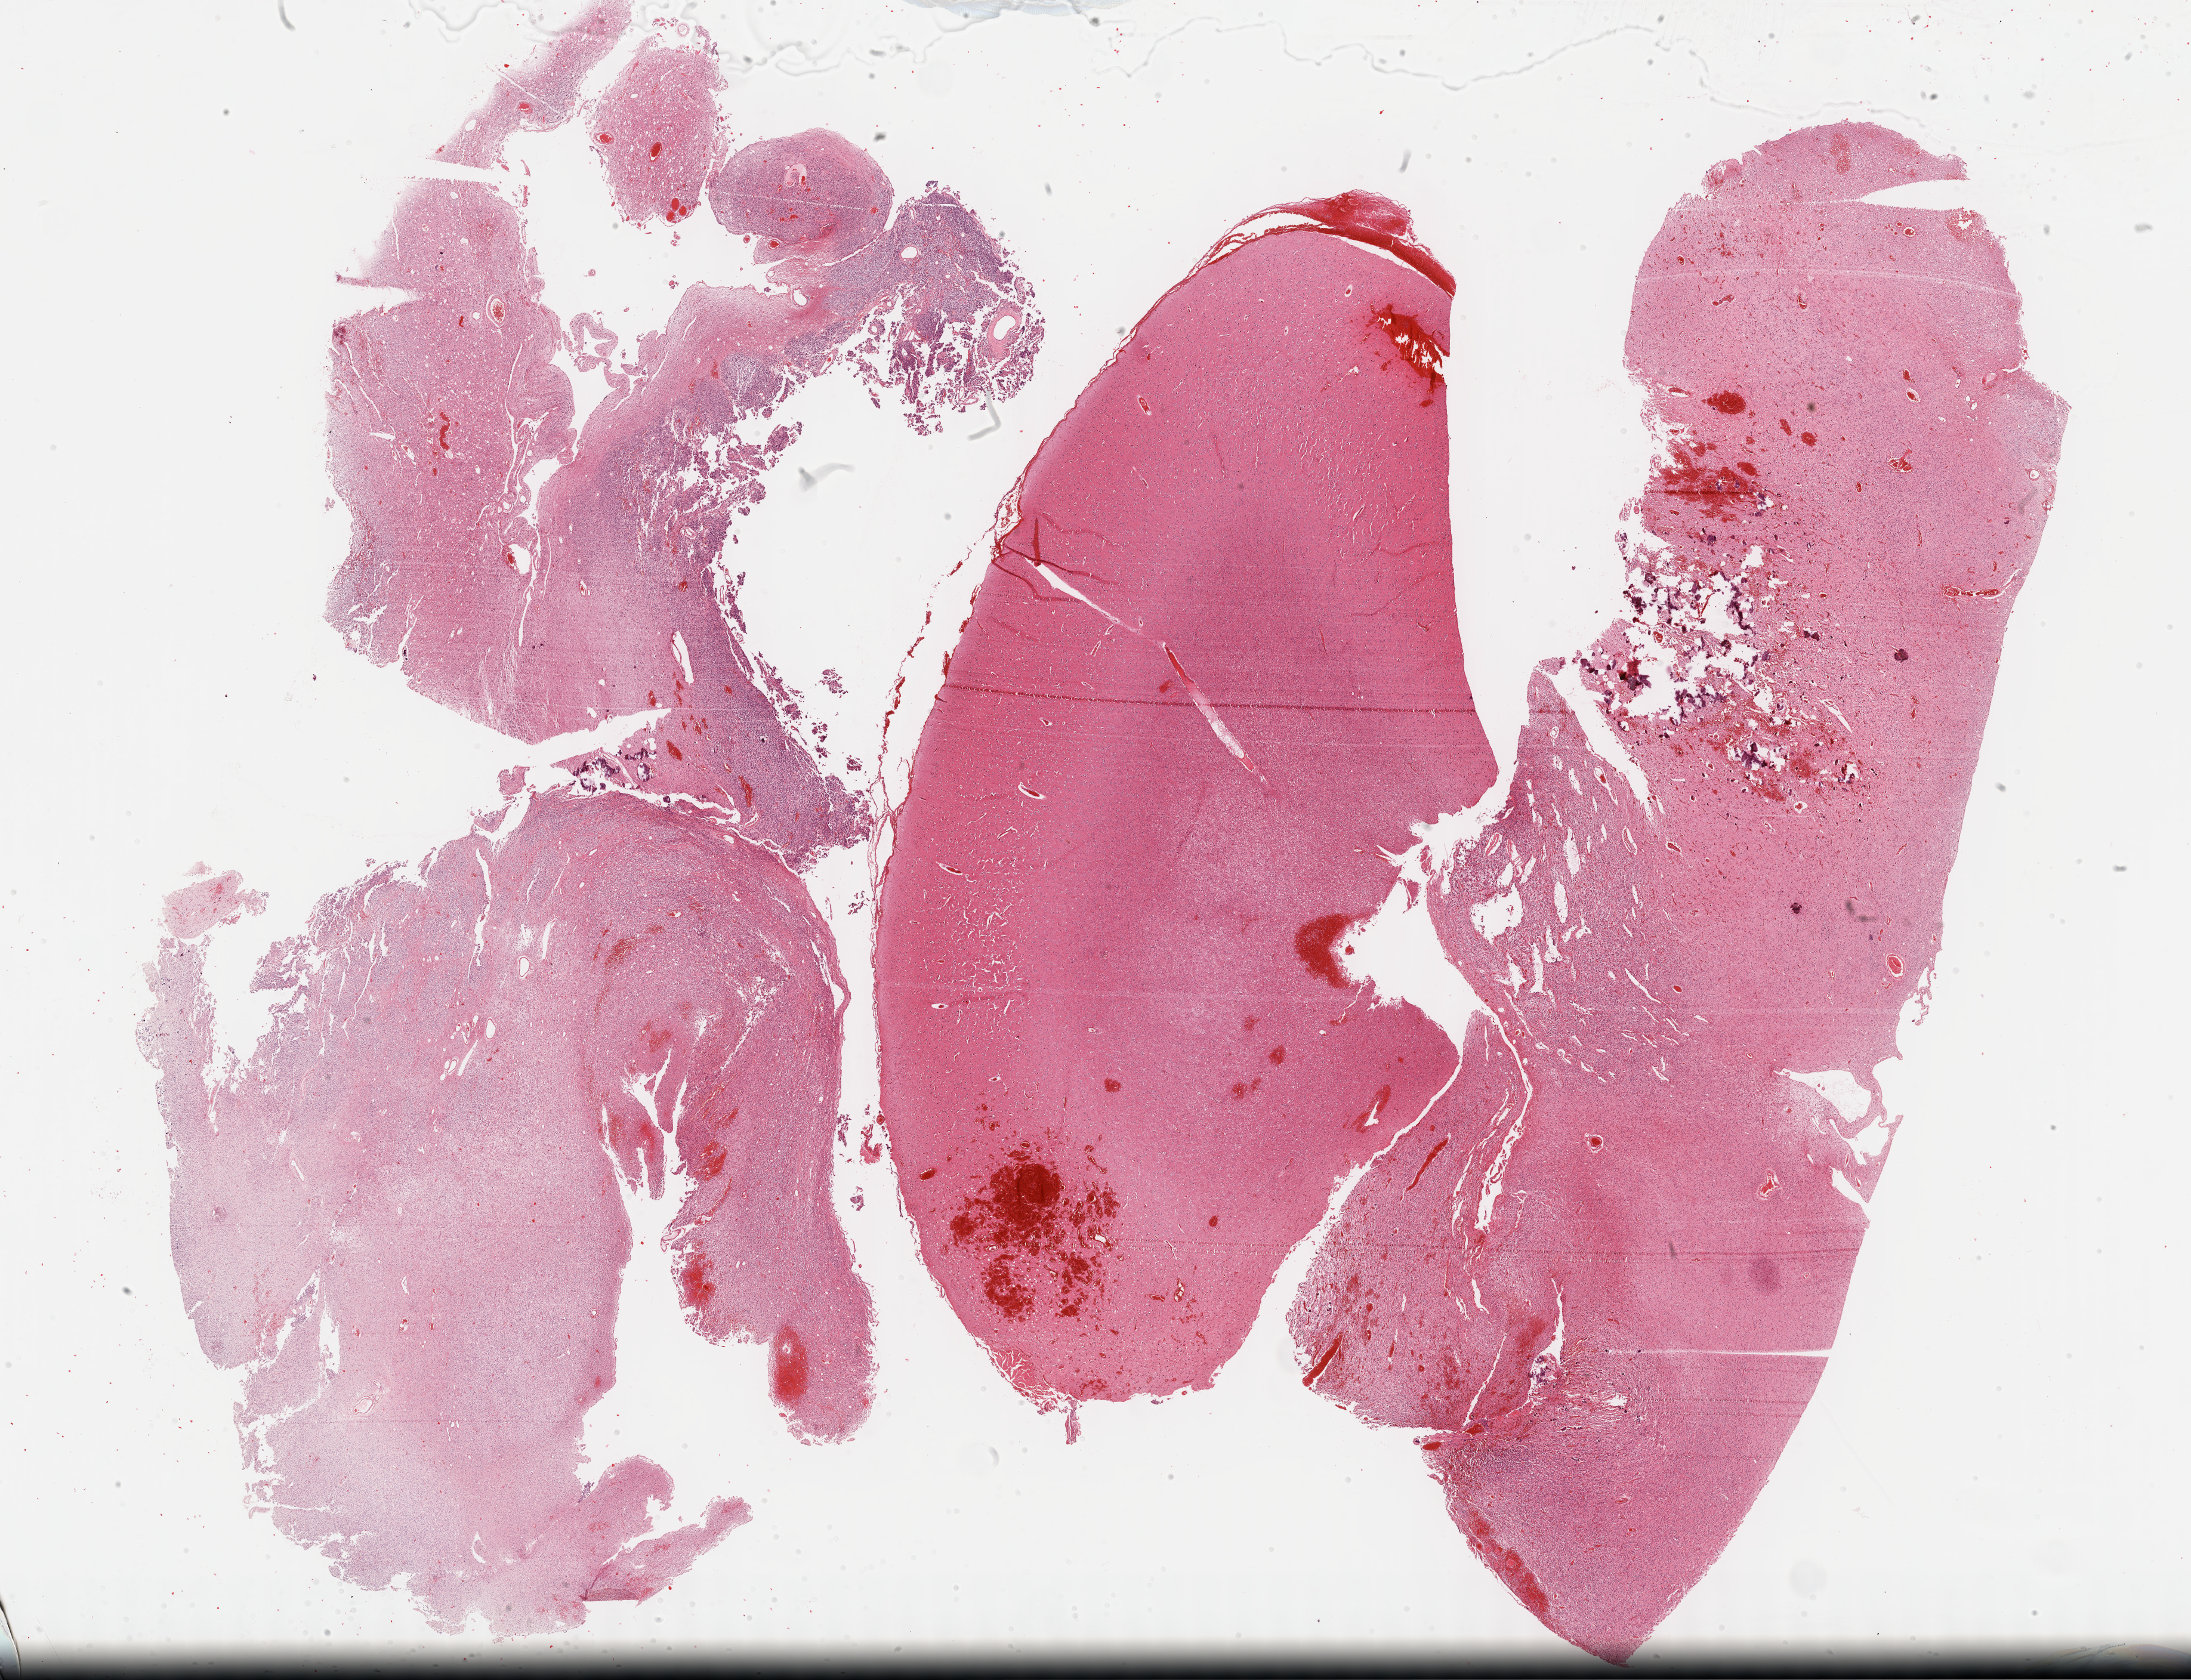
Whole-slide histology image, H&E-stained, a low-resolution overview of the entire scanned area, about 29.7 x 22.8 mm (slide scanned at 40x). Formalin-fixed paraffin-embedded (FFPE) diagnostic section. Sample: primary tumour, brain. Male patient; age at initial diagnosis 35 years. Histologic grade: G2 (moderately differentiated).
Diagnosis: Oligodendroglioma, NOS (cerebrum). Laterality: midline.